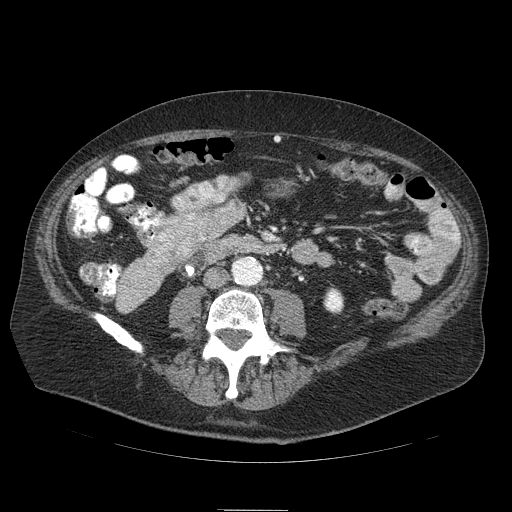
Contrast-enhanced abdominal CT (liver protocol), one axial slice. Position 11 of 103 along the scan axis. Reconstruction kernel STANDARD. 120 kVp. Soft-tissue window (W 400 / L 40 HU). 2.5 mm slice thickness. 512 × 512 image matrix. From the clinical record (not read from this slice): diagnosis: hepatocellular carcinoma (patient treated with transarterial chemoembolisation; whether this scan precedes or follows treatment is not stated here); TNM stage (as recorded): Stage-IIIA; Child-Pugh class: B; tumour differentiation: well differentiated; tumour nodularity: multinodular.
Structures marked on this image (semi-automatic segmentation, software-assisted and operator-edited):
- mass: box from (x=147, y=198) to (x=244, y=268) px